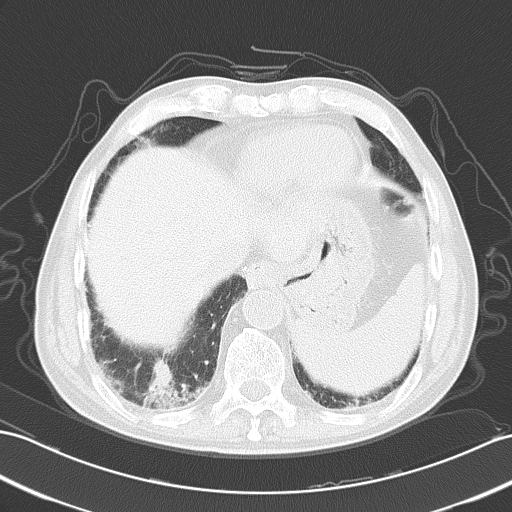
Chest CT, one axial slice. Position 12 of 51 along the scan axis. Reconstruction kernel B70f. 120 kVp. Lung window (W 1500 / L -600 HU). 5 mm slice thickness. 512 × 512 image matrix, field of view 353 × 353 mm. Male patient, age 73 years. From the clinical record (not read from this slice): clinical TNM (as recorded): T1a N0 M0; histopathological grade: G3.
Outlined on this slice (bounding box drawn by a radiologist):
- lung tumour (recorded histology: small cell carcinoma): bounding box [x1, y1, x2, y2] px = [134, 354, 181, 398]